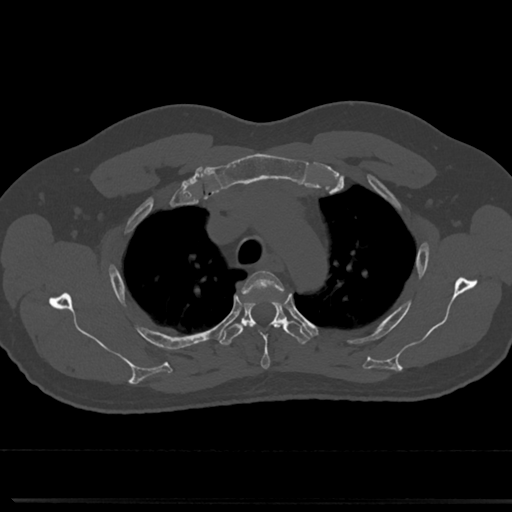
CT including the spine, one axial slice; position 566 of 817 along the scan axis; 120 kVp; bone window (W 1800 / L 400 HU); 0.5 mm slice thickness; 512 × 512 image matrix, field of view 355 × 355 mm. Patient: male, 61 years. From the clinical record (not read from this slice): primary cancer: prostate.
Annotated regions visible in this slice (semi-automatic segmentation, software-assisted and operator-edited):
- T3 vertebra: bounding box (x1, y1, x2, y2) in pixels: (244, 270, 291, 369)
- T4 vertebra: (219, 299, 311, 346)